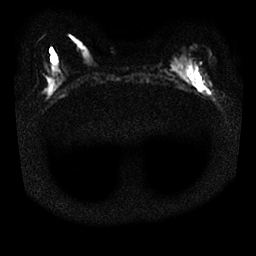
Breast MRI, one axial slice. Position 9 of 25 along the scan axis. Diffusion-weighted series; image 2 of 4 stored at this slice position (different b-values; order by instance number). 1.5 T. 4 mm slice thickness. 256 × 256 image matrix. Female patient.
Structures marked on this image (outlined manually by an expert reader):
- tumour on diffusion-weighted imaging: box from (x=190, y=75) to (x=211, y=95) px